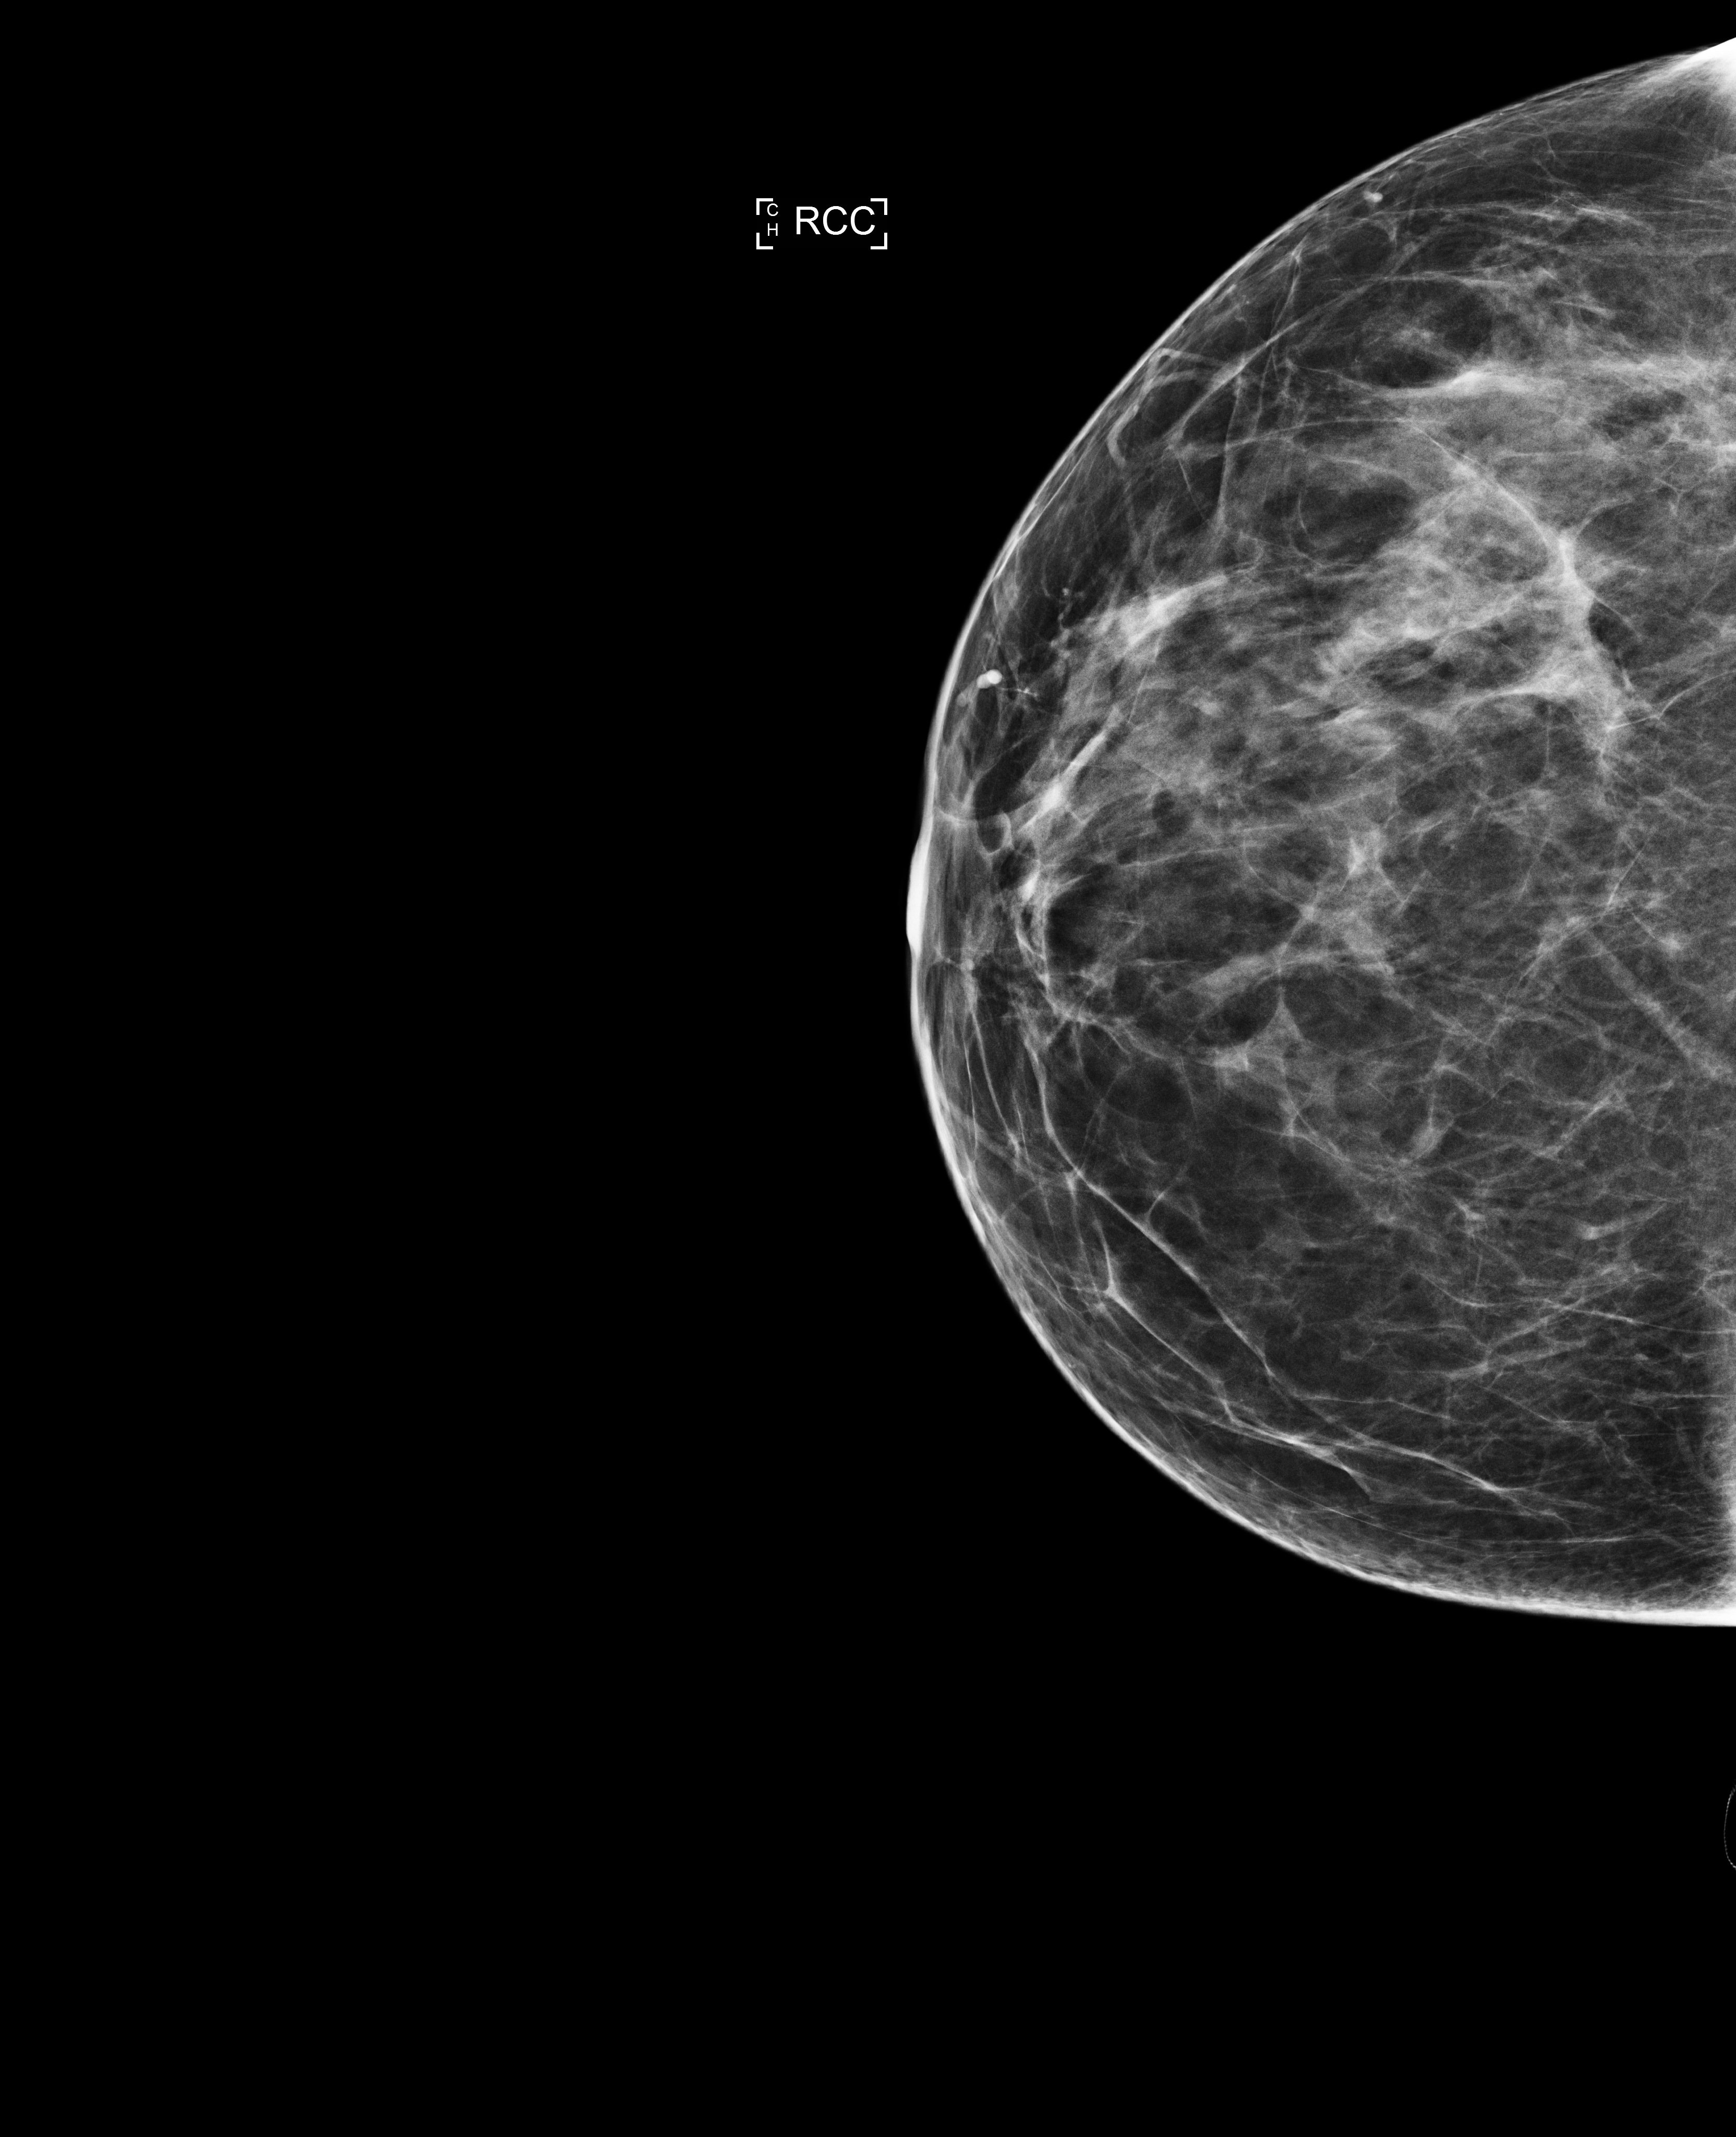
Digital mammogram (FFDM), right breast, CC view, annual screening mammography examination, compressed breast thickness 62 mm. Patient aged 40 years (female).
- BI-RADS breast density category at the screening exam (both breasts, scale 1–4): 2
- final BI-RADS assessment for this screening round (tomosynthesis exam, both breasts): category 1
- recall: no recall after this screen